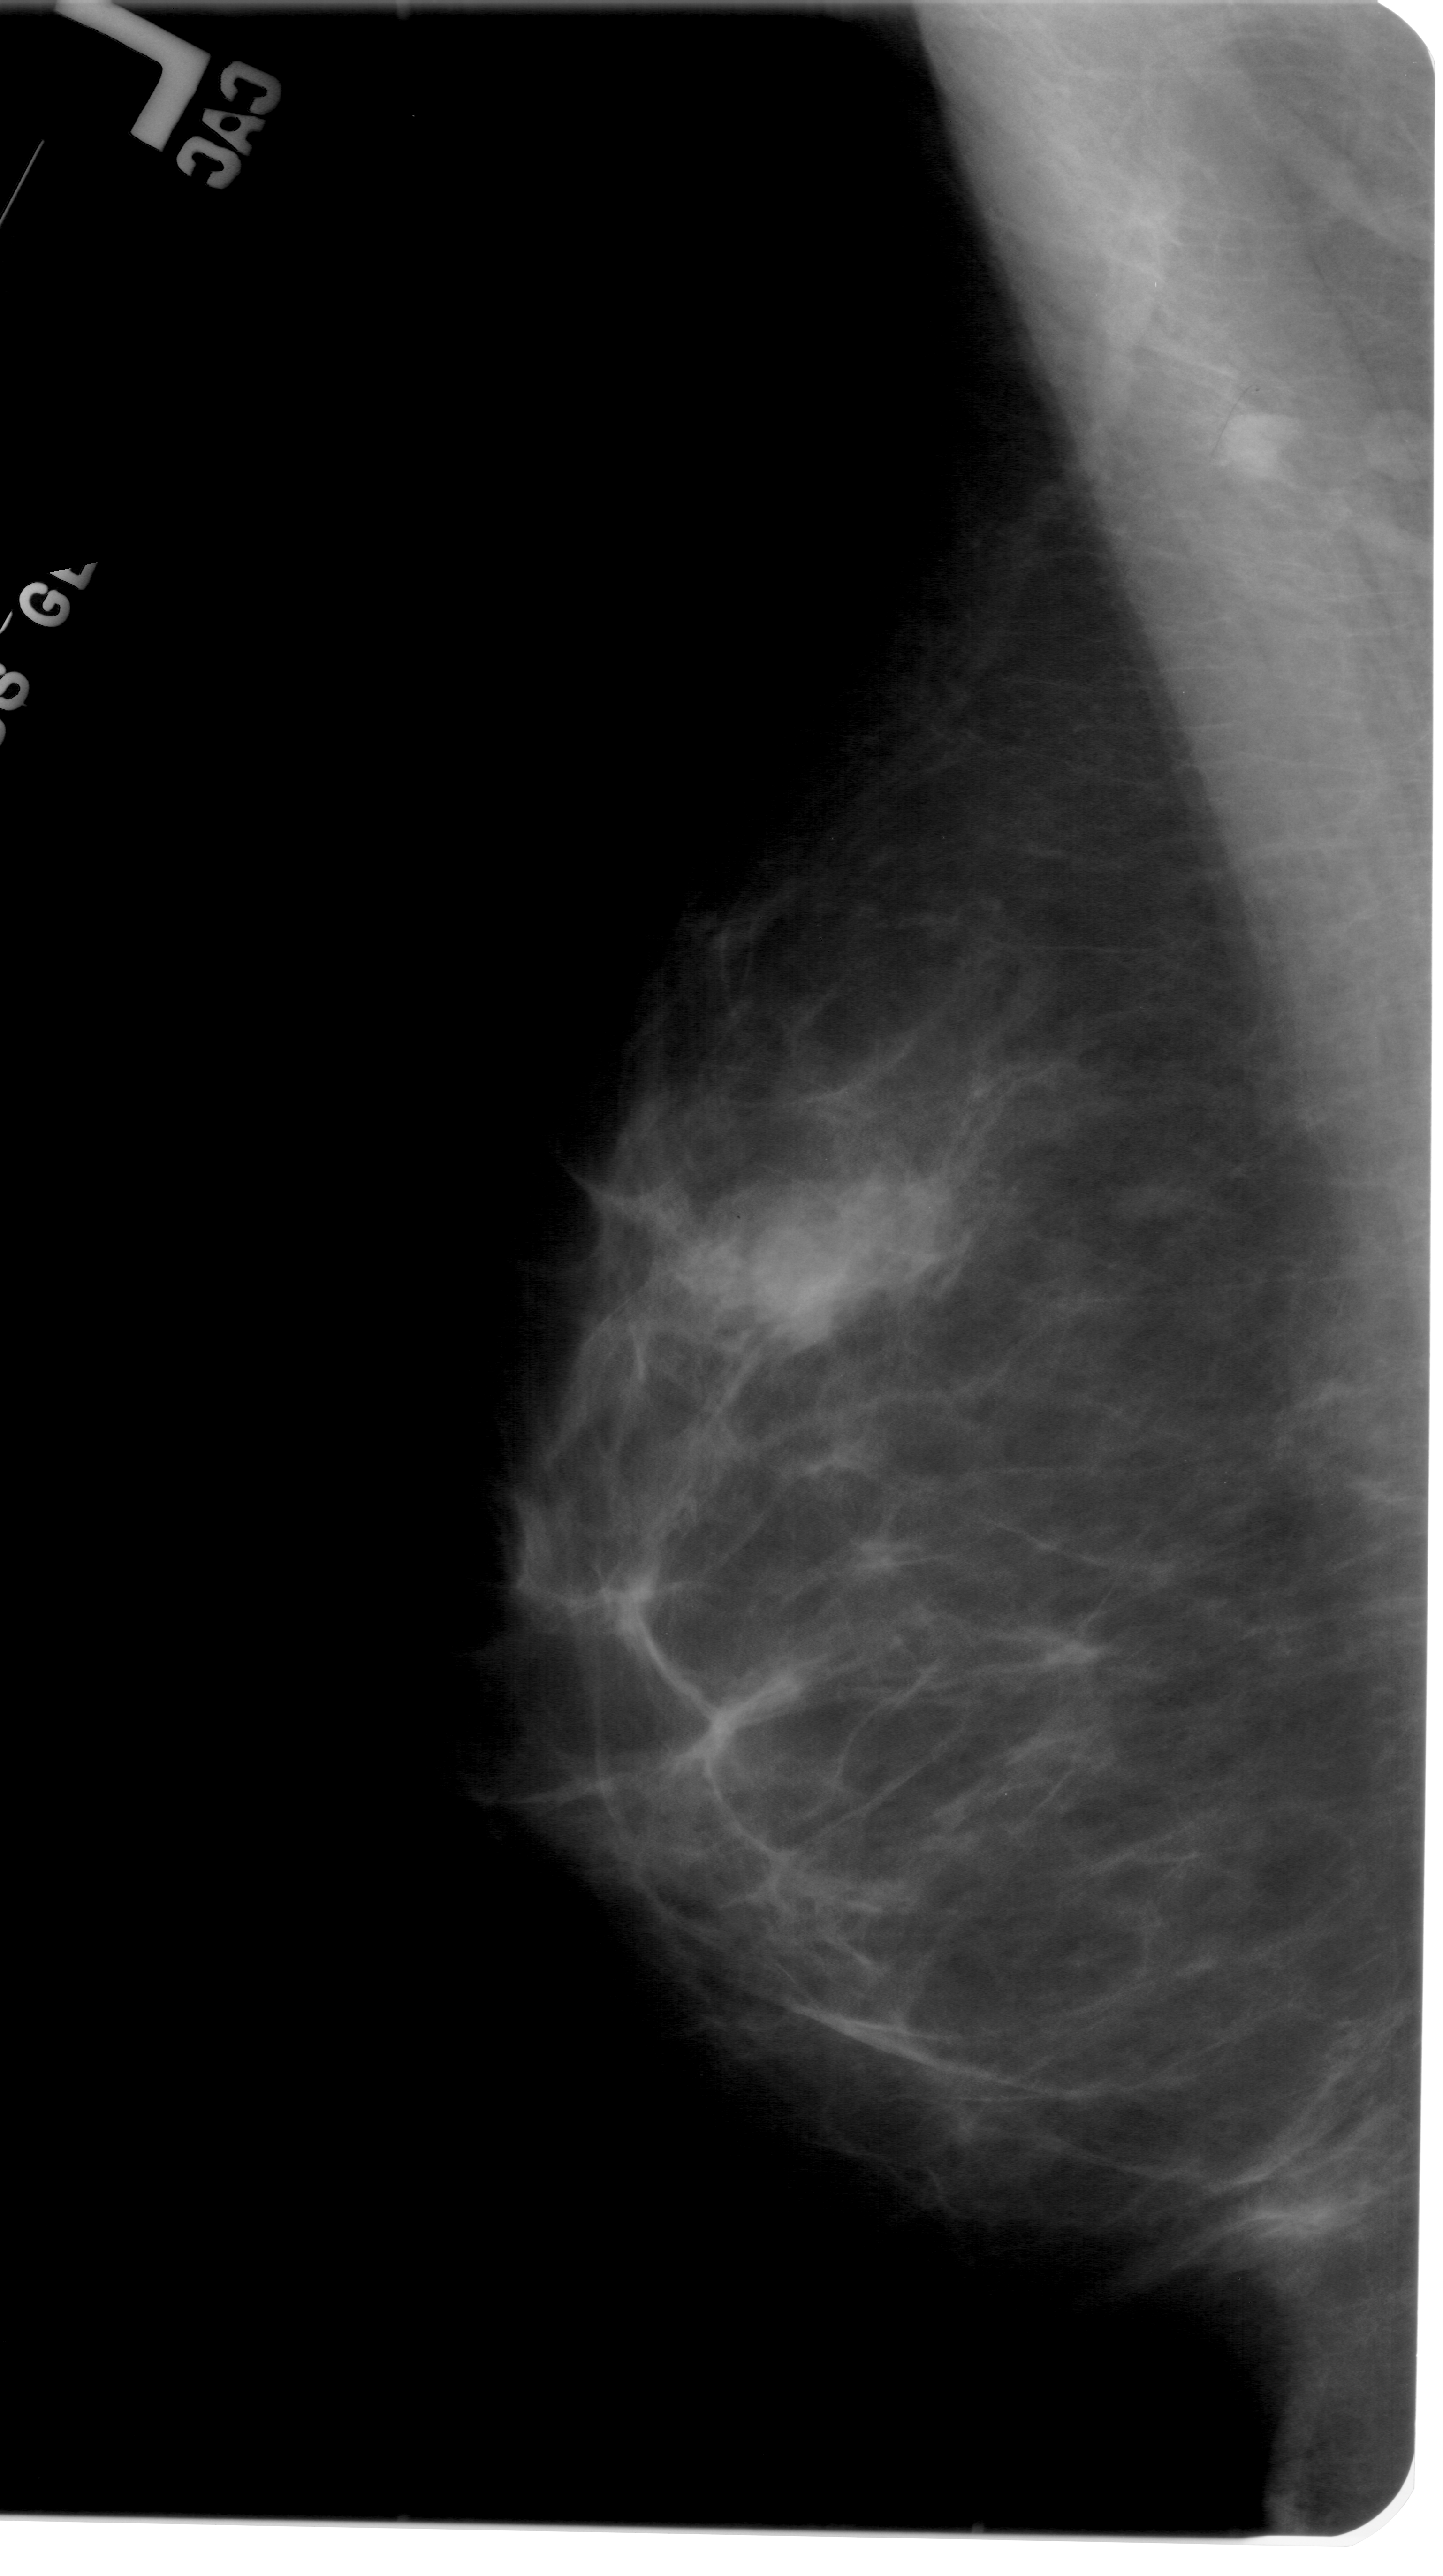
Scanned film-screen mammogram; left breast; MLO view; BI-RADS breast density category 1 (scale 1–4).
Radiologist-marked abnormalities on this image: mass, shape lobulated, margins obscured; BI-RADS assessment category 3; subtlety rating 3 on a 1 (subtle) to 5 (obvious) scale; pathology (as recorded): benign.